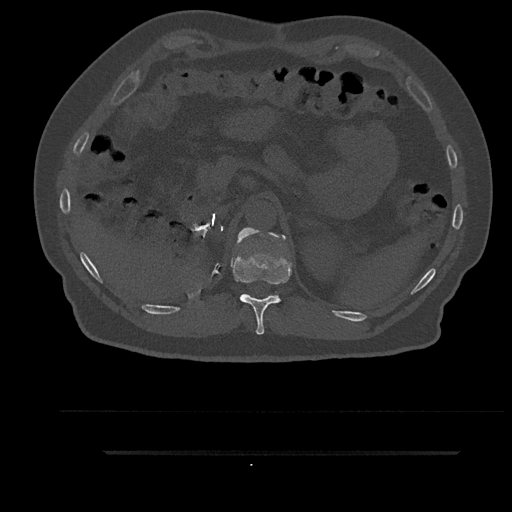
CT including the spine, one axial slice. Position 286 of 797 along the scan axis. Reconstruction kernel Br40s/3. Bone window (W 1800 / L 400 HU). 512 × 512 image matrix, field of view 432 × 432 mm. Patient: male, 63 years. Case-level facts recorded for this patient, not image findings: primary cancer: renal.
Structures marked on this image (semi-automatically segmented with operator editing):
- T11 vertebra: box from (x=231, y=228) to (x=292, y=335) px
- T12 vertebra: (x=236, y=227)–(x=285, y=245)